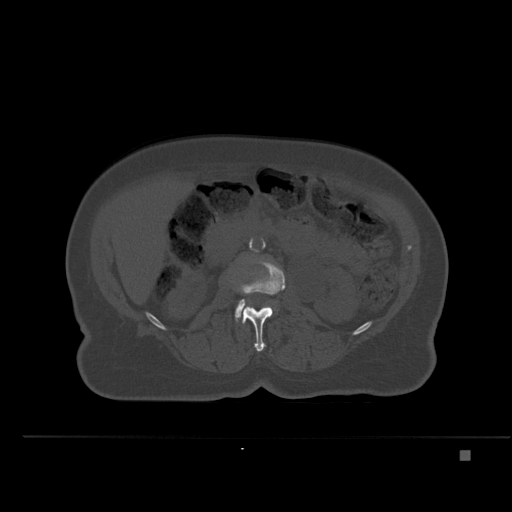
CT including the spine, one axial slice. Position 211 of 477 along the scan axis. Bone window (W 1800 / L 400 HU). 1.5 mm slice thickness. 512 × 512 image matrix, field of view 422 × 422 mm. Patient: female, 74 years. From the clinical record (not read from this slice): primary cancer: colon.
Structures marked on this image (semi-automatically segmented with operator editing):
- L2 vertebra: bounding box (x1, y1, x2, y2) in pixels: (237, 260, 285, 352)
- L3 vertebra: (235, 299, 246, 319)